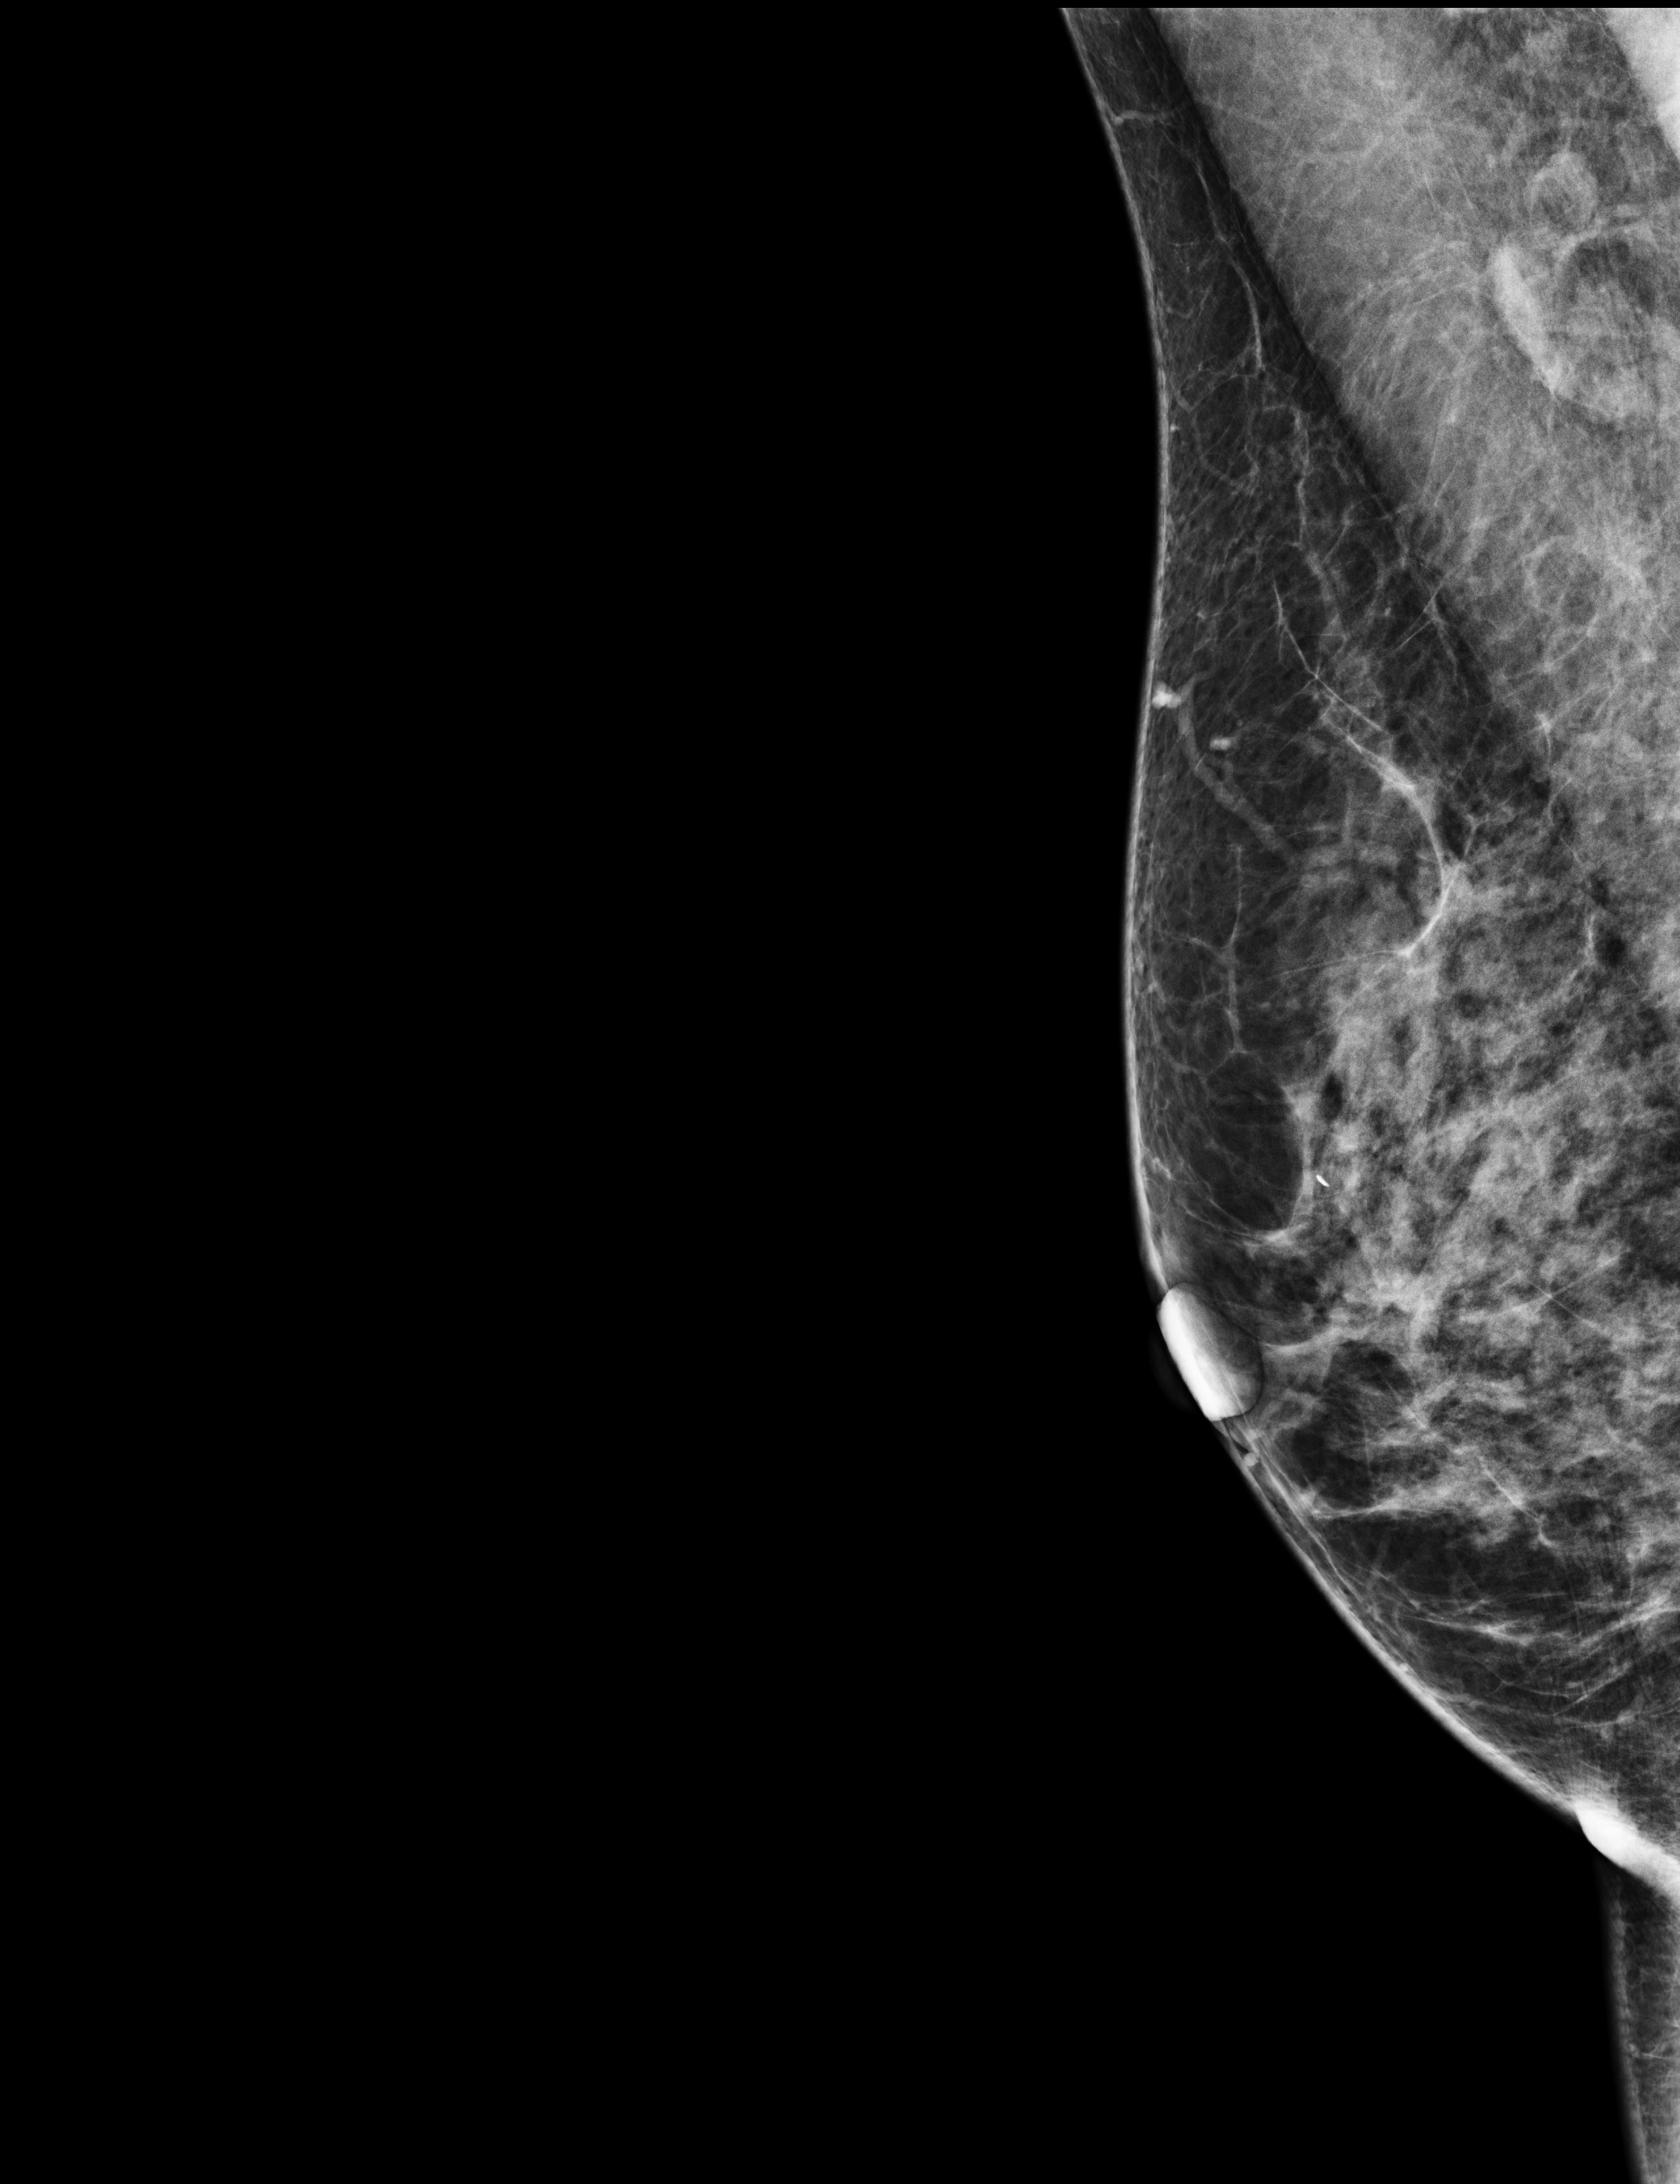
Full-field digital mammogram (FFDM), right breast, mediolateral oblique (MLO) view, annual screening mammography examination, system: Selenia Dimensions. Female patient, age 54 years.
- BI-RADS breast density category at the screening exam (both breasts, scale 1–4): 3
- final BI-RADS category for the screening round (tomosynthesis exam, both breasts): category 1
- recall: no recall after this screen